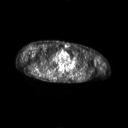
FDG PET of an extremity soft-tissue mass (from a PET/CT study), one axial slice. 3.27 mm slice thickness. 128 × 128 image matrix. Male patient, age 61 years. Case-level facts recorded for this patient, not image findings: histological type: pleiomorphic spindle cell undifferentiated; grade: high; site of the primary tumour: right parascapusular.
Annotated regions visible in this slice (expert contour drawn on MRI and transferred to this co-registered scan by the dataset authors):
- gross tumour volume including surrounding oedema: bounding box <35,70,59,78> (left, top, right, bottom; pixels)
- gross tumour volume (mass): <40,70,47,75>